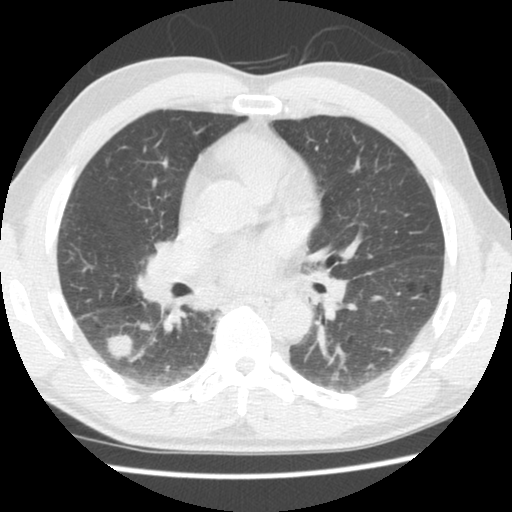
Low-dose screening chest CT, one axial slice; position 79 of 133 along the scan axis; reconstruction kernel STANDARD; lung window (W 1500 / L -600 HU); 2.5 mm slice thickness; 512 × 512 image matrix.
Outlined on this slice (expert manual segmentation):
- lesion 1 (tumor, lower lobe of right lung): bounding box (x1, y1, x2, y2) in pixels: (106, 335, 134, 359)